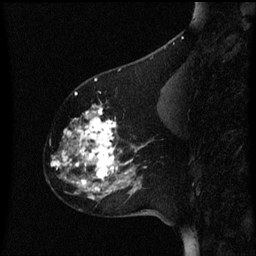
Breast MRI (dynamic contrast-enhanced), one sagittal slice; position 23 of 60 along the scan axis; dynamic contrast-enhanced series, image 2 of 3 at this slice position (ordered by acquisition); 1.5 T; TE 4.2 ms, TR 8 ms; 2 mm slice thickness; 256 × 256 image matrix, field of view 200 × 200 mm. Female patient, age 60 years.
Annotated regions visible in this slice (semi-automatically segmented with operator editing):
- analysis volume of interest (the breast-tissue region the enhancement analysis was run in; not a lesion): bounding box (x1, y1, x2, y2) in pixels: (49, 100, 151, 197)
- tumour enhancement mask (voxels above the 70 % enhancement threshold inside the analysis volume of interest): (51, 108, 147, 195)